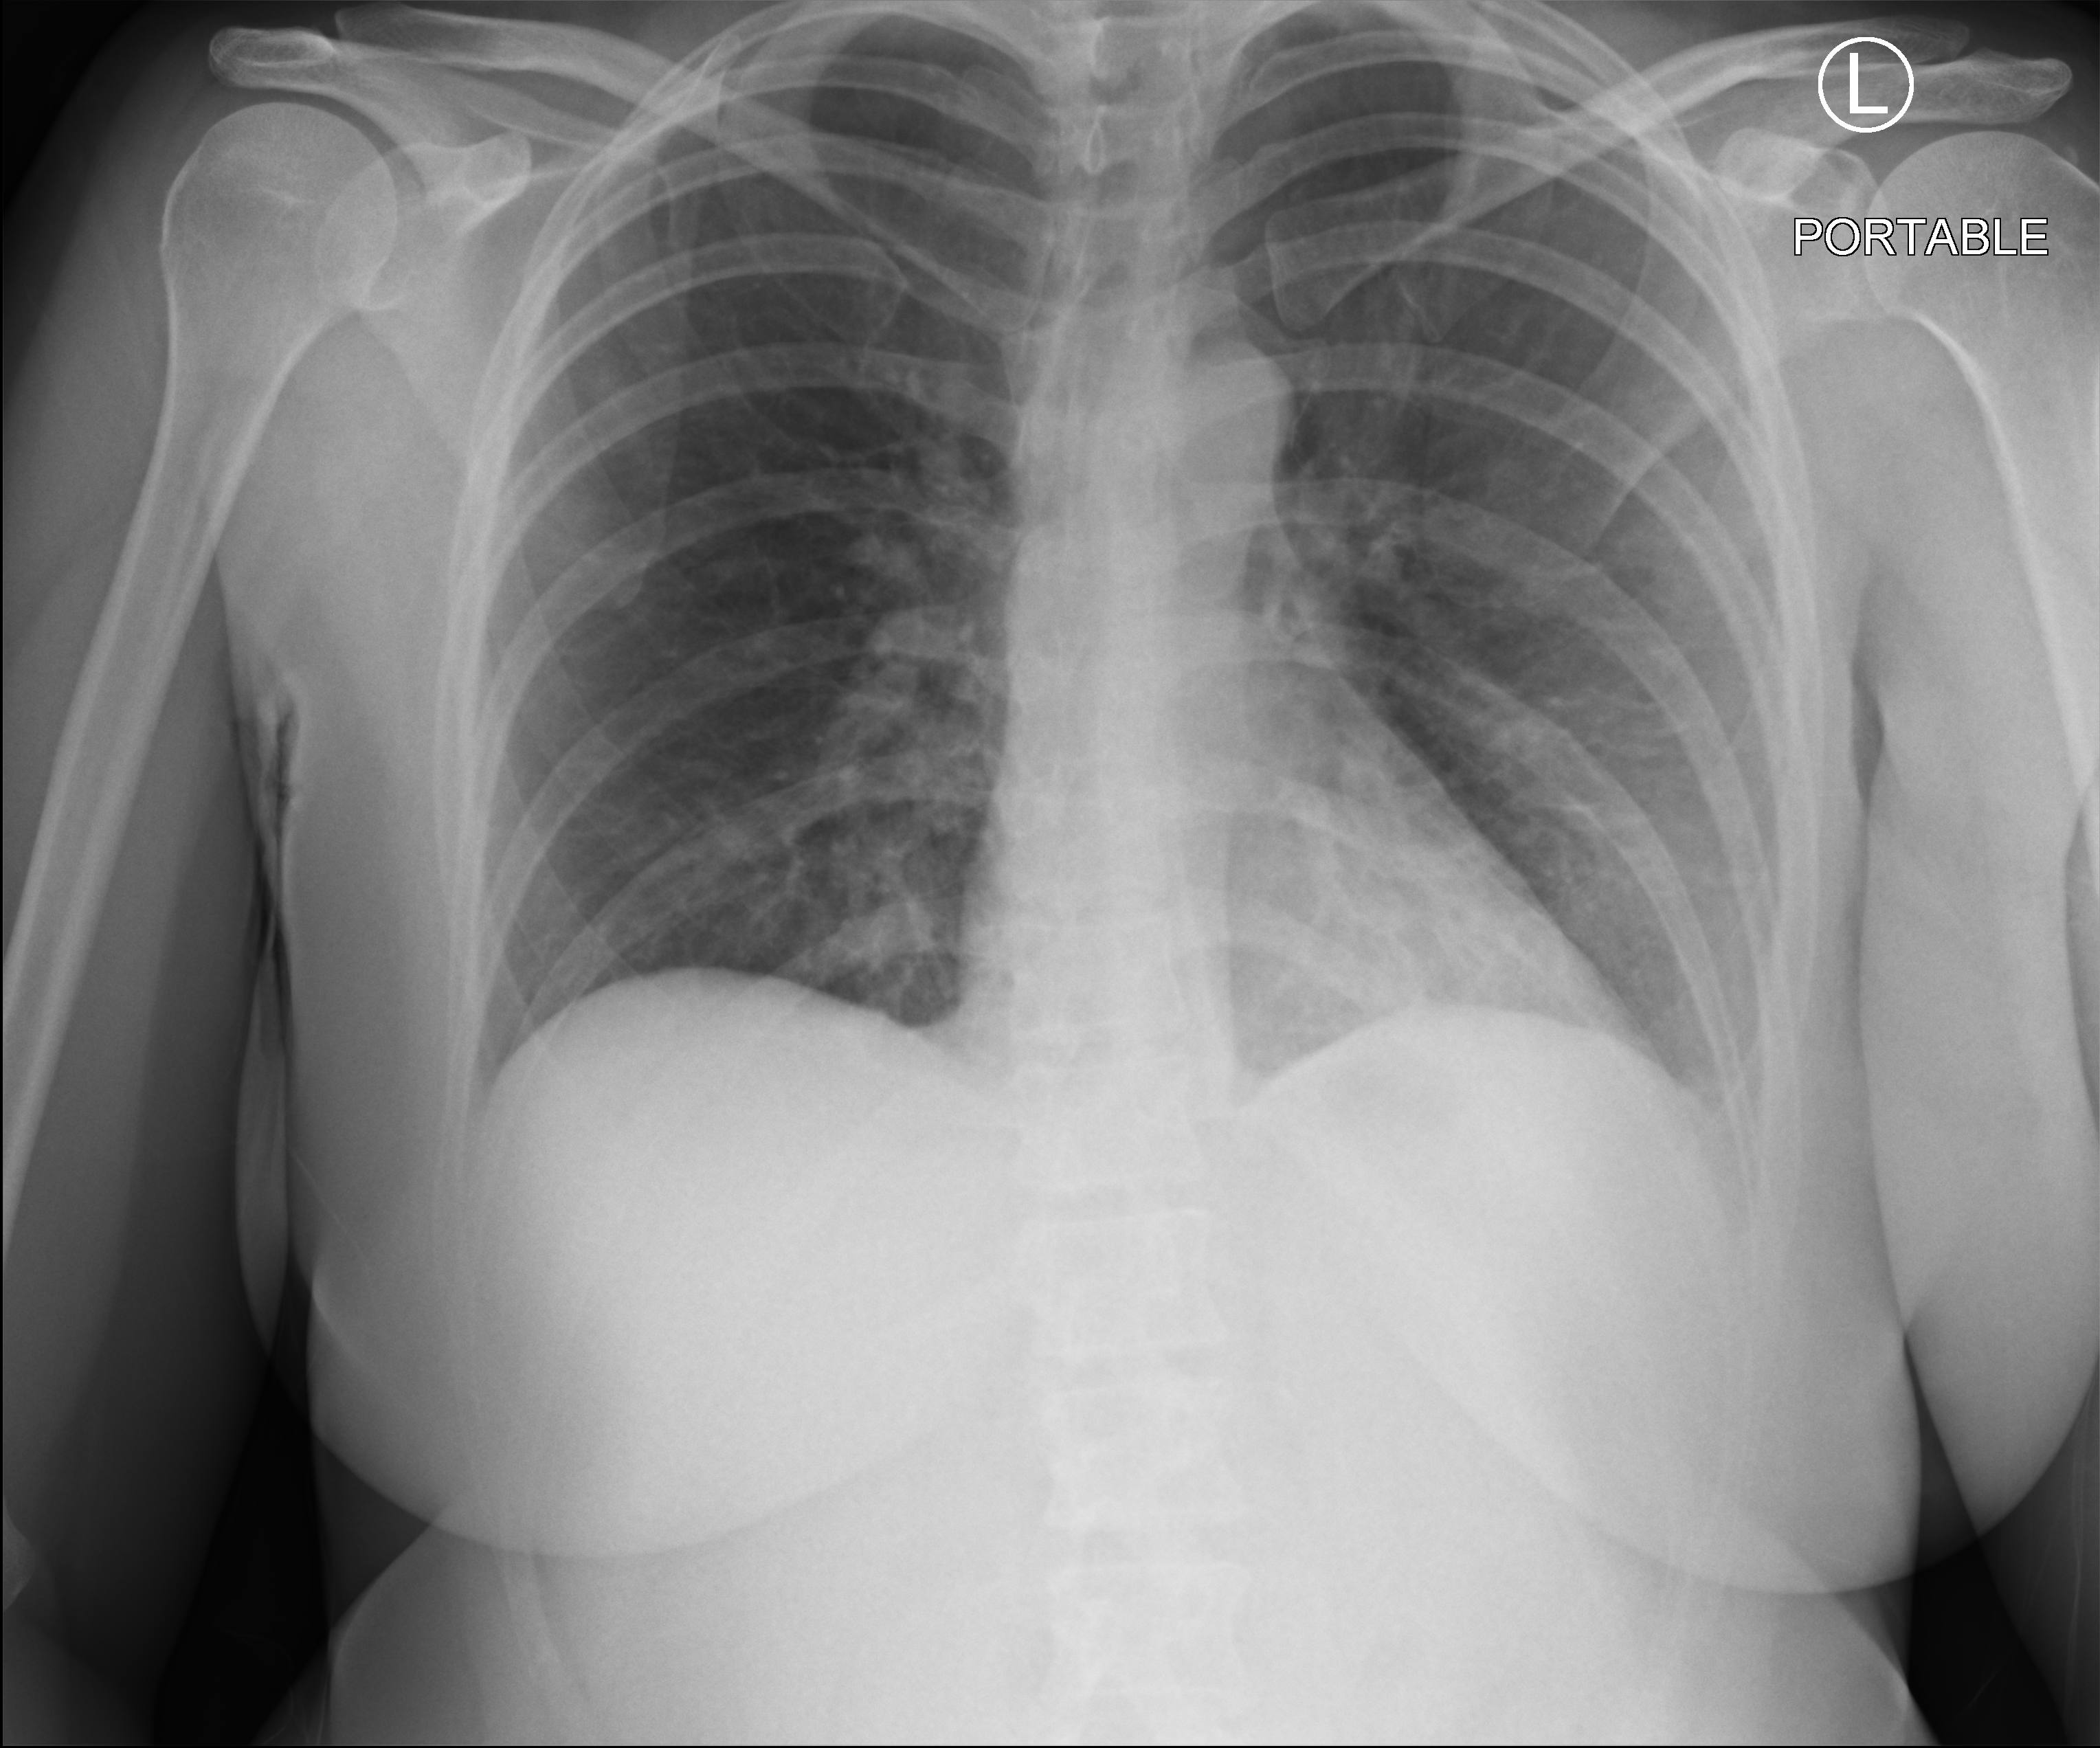
Chest X-ray (portable). Patient hospitalised with COVID-19; female, aged 18–59 years.
Hospital-stay facts (about this admission, not read from this image; timing relative to this image not recorded): hypertension (admission record): no.